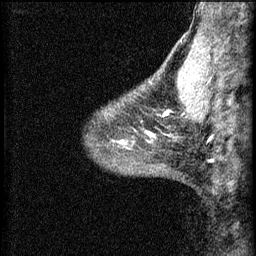
Breast MRI (dynamic contrast-enhanced), one sagittal slice. Position 18 of 60 along the scan axis. 3 images stored at this slice position (order not interpretable as contrast timing). 1.5 T. TE 4.2 ms, TR 8.2 ms. 2.2 mm slice thickness. 256 × 256 image matrix, field of view 180 × 180 mm. Female patient, age 40 years.
Structures marked on this image (semi-automatically segmented with operator editing):
- analysis volume of interest (the breast-tissue region the enhancement analysis was run in; not a lesion): bounding box (x1, y1, x2, y2) in pixels: (108, 88, 173, 139)
- tumour enhancement mask (voxels above the 70 % enhancement threshold inside the analysis volume of interest): (166, 112, 169, 115)